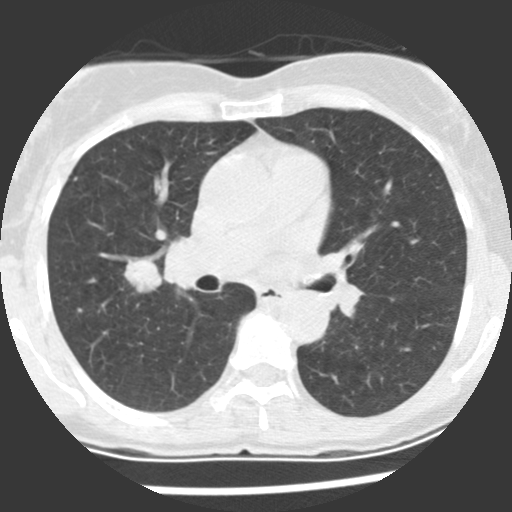
Low-dose screening chest CT, axial slice. First (baseline) screen. Lung window (W 1500 / L -600 HU). 2.5 mm slice thickness. Standard (soft-tissue) reconstruction kernel (STANDARD). 120 kVp. Female participant, aged 60 years at enrolment. Current smoker at enrolment.
Expert-annotated lung lesion, box from (x=115, y=254) to (x=172, y=300) px. The screening reader recorded 2 non-calcified nodules or masses ≥4 mm on this exam (right upper lobe, right middle lobe); which of them this box marks is not recorded.